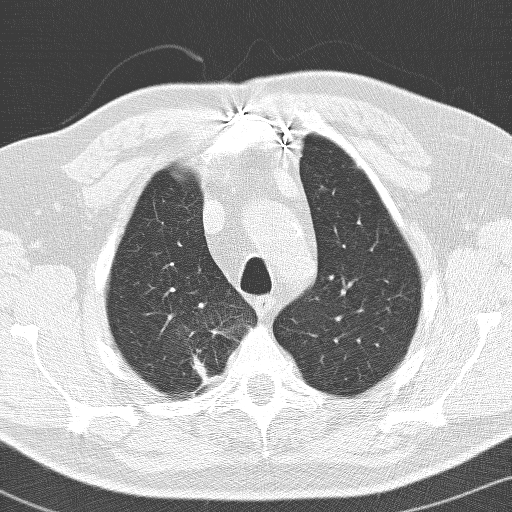
Chest CT (low-dose screening protocol), one axial image; baseline annual screen; lung window (W 1500 / L -600 HU); lung (sharp) reconstruction kernel (D); slice 24 of 141 in the series. Male participant, aged 66 years at enrolment. Former smoker at enrolment.
Expert reader's lesion annotation, box from (x=156, y=320) to (x=231, y=394) px. Screening reader's record for this exam (one nodule recorded; not confirmed to be the boxed lesion): non-calcified nodule or mass ≥4 mm, right upper lobe, 36 × 30 mm, spiculated (stellate) margins, soft tissue attenuation. Official screen result: positive, change unspecified: nodule(s) >= 4 mm or enlarging nodule(s), mass(es), or other non-specific abnormalities suspicious for lung cancer.